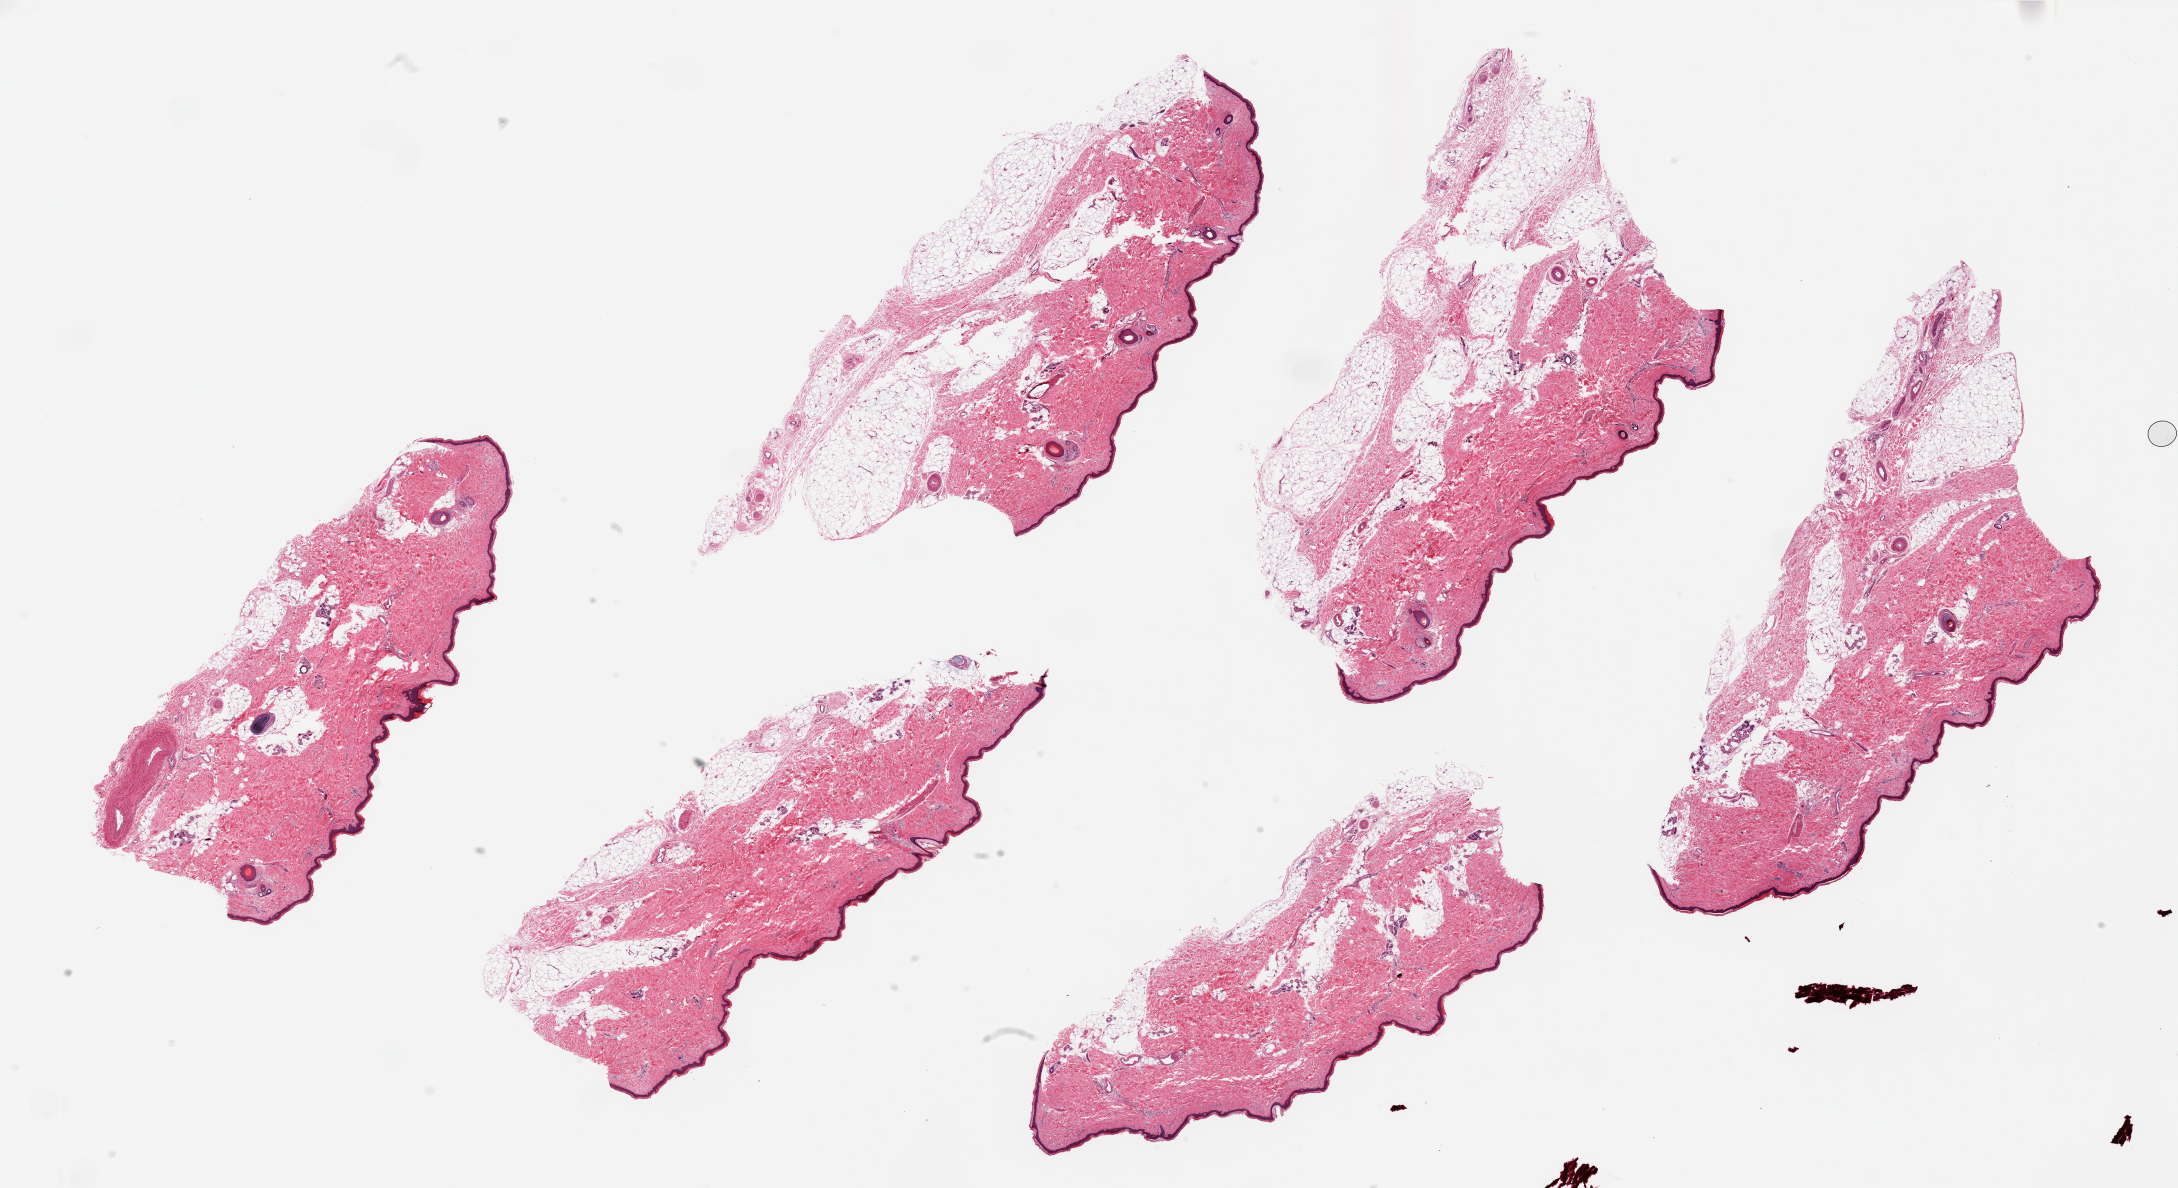
Digitized haematoxylin and eosin-stained section, brightfield, a low-resolution overview of the entire scanned area, about 34.5 x 18.8 mm (acquisition: 20x scan). PAXgene-fixed paraffin-embedded (PFPE) section. Section of skin of lower leg (target tissue). Donor tissue sample. Donor: male.
Review note (as recorded): 6 pieces, up to 11x5.5; up to 2 mm thick band of subcutaneous adipose tissue.